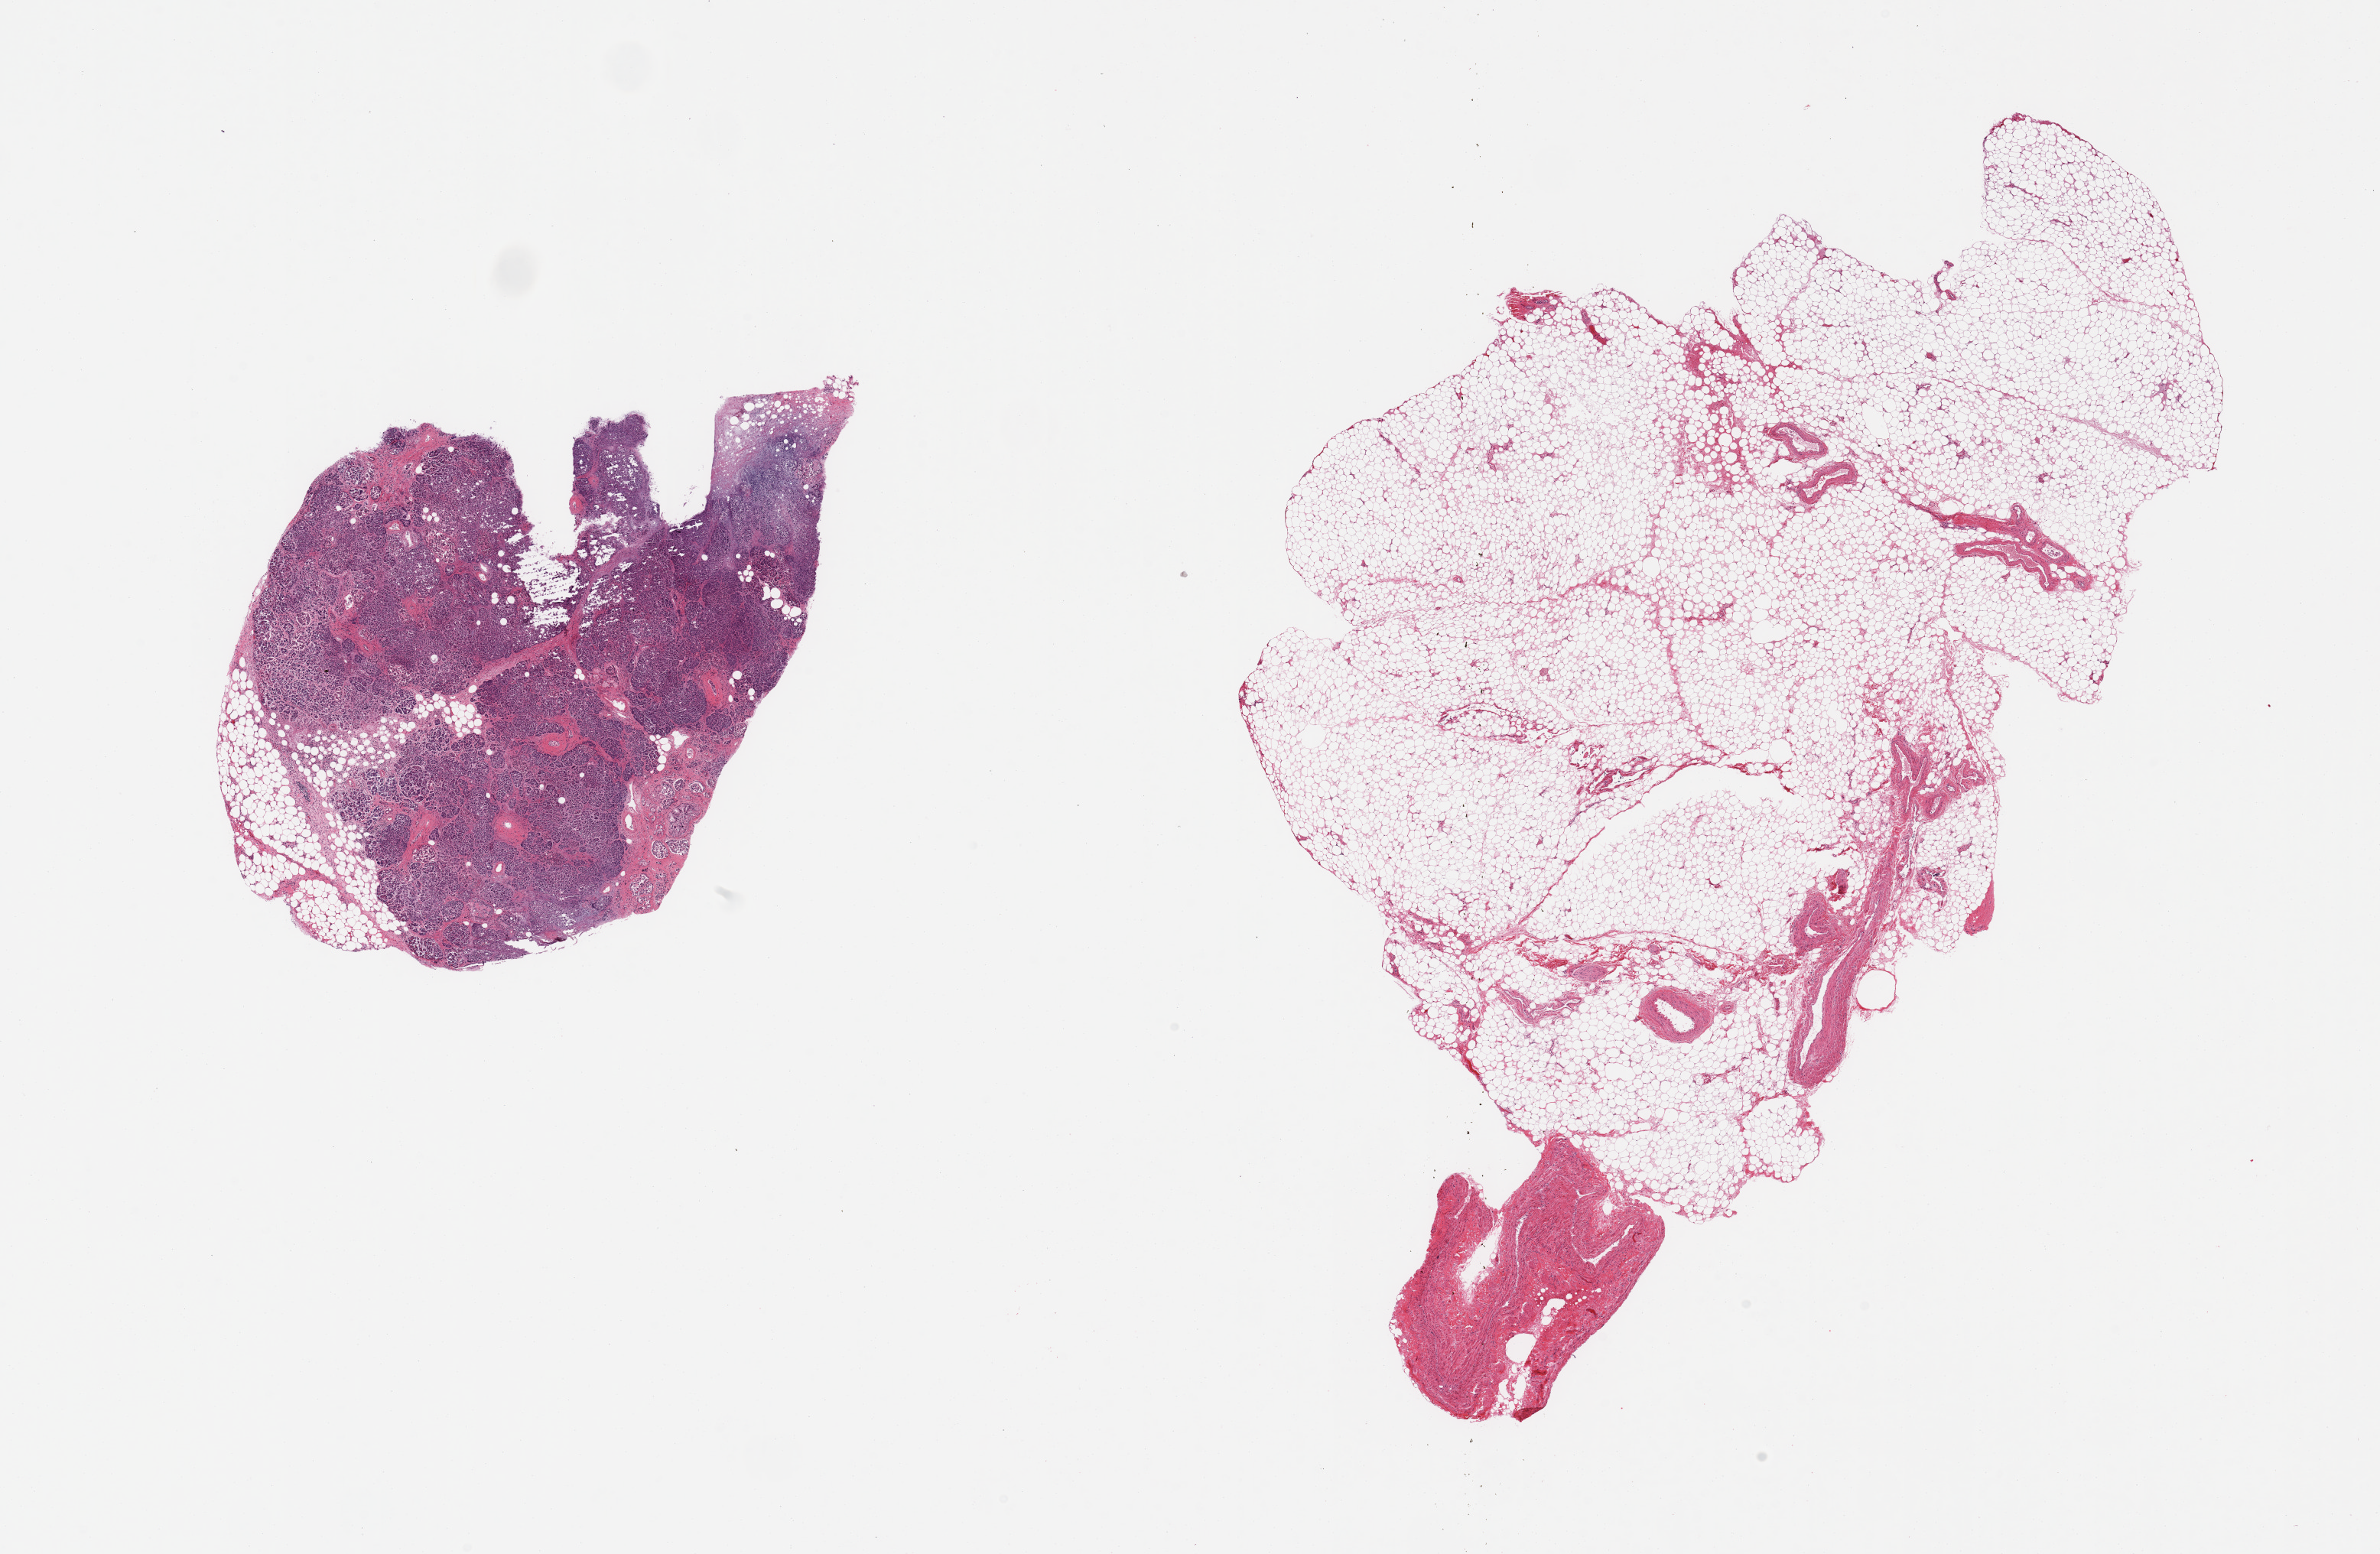
H&E whole-slide image, a low-resolution overview of the entire scanned area, about 24.6 x 16.1 mm; PAXgene-fixed paraffin-embedded (PFPE) section; section of pancreas (target tissue); tissue donor sample. Donor sex: male.
* pathologist's review note for this sample: 2 pieces; 1 piece is pancreas with focal fibrosis & 25% fat content; other piece has 90% fat, 10% fibrovascular content with no pancreatic tissue